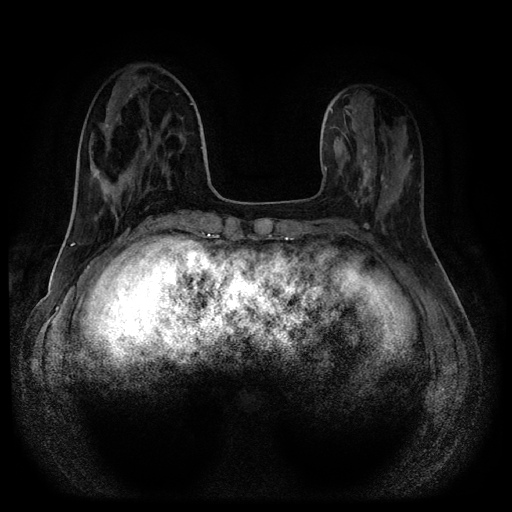
Breast MRI (dynamic contrast-enhanced, multi-phase), one axial slice; slice 36 of 116 in the series (ordered by position); dynamic contrast-enhanced series, time point 2 of 5 at this slice position (early post-contrast); 1.5 T; TE 2.7 ms, TR 5.4 ms; 512 × 512 image matrix, field of view 340 × 340 mm. Patient: female, 40 years.
Annotated regions visible in this slice (semi-automatically segmented with operator editing):
- breast lesion (labelled benign in the annotation): bounding box (x1, y1, x2, y2) in pixels: (351, 136, 377, 208)